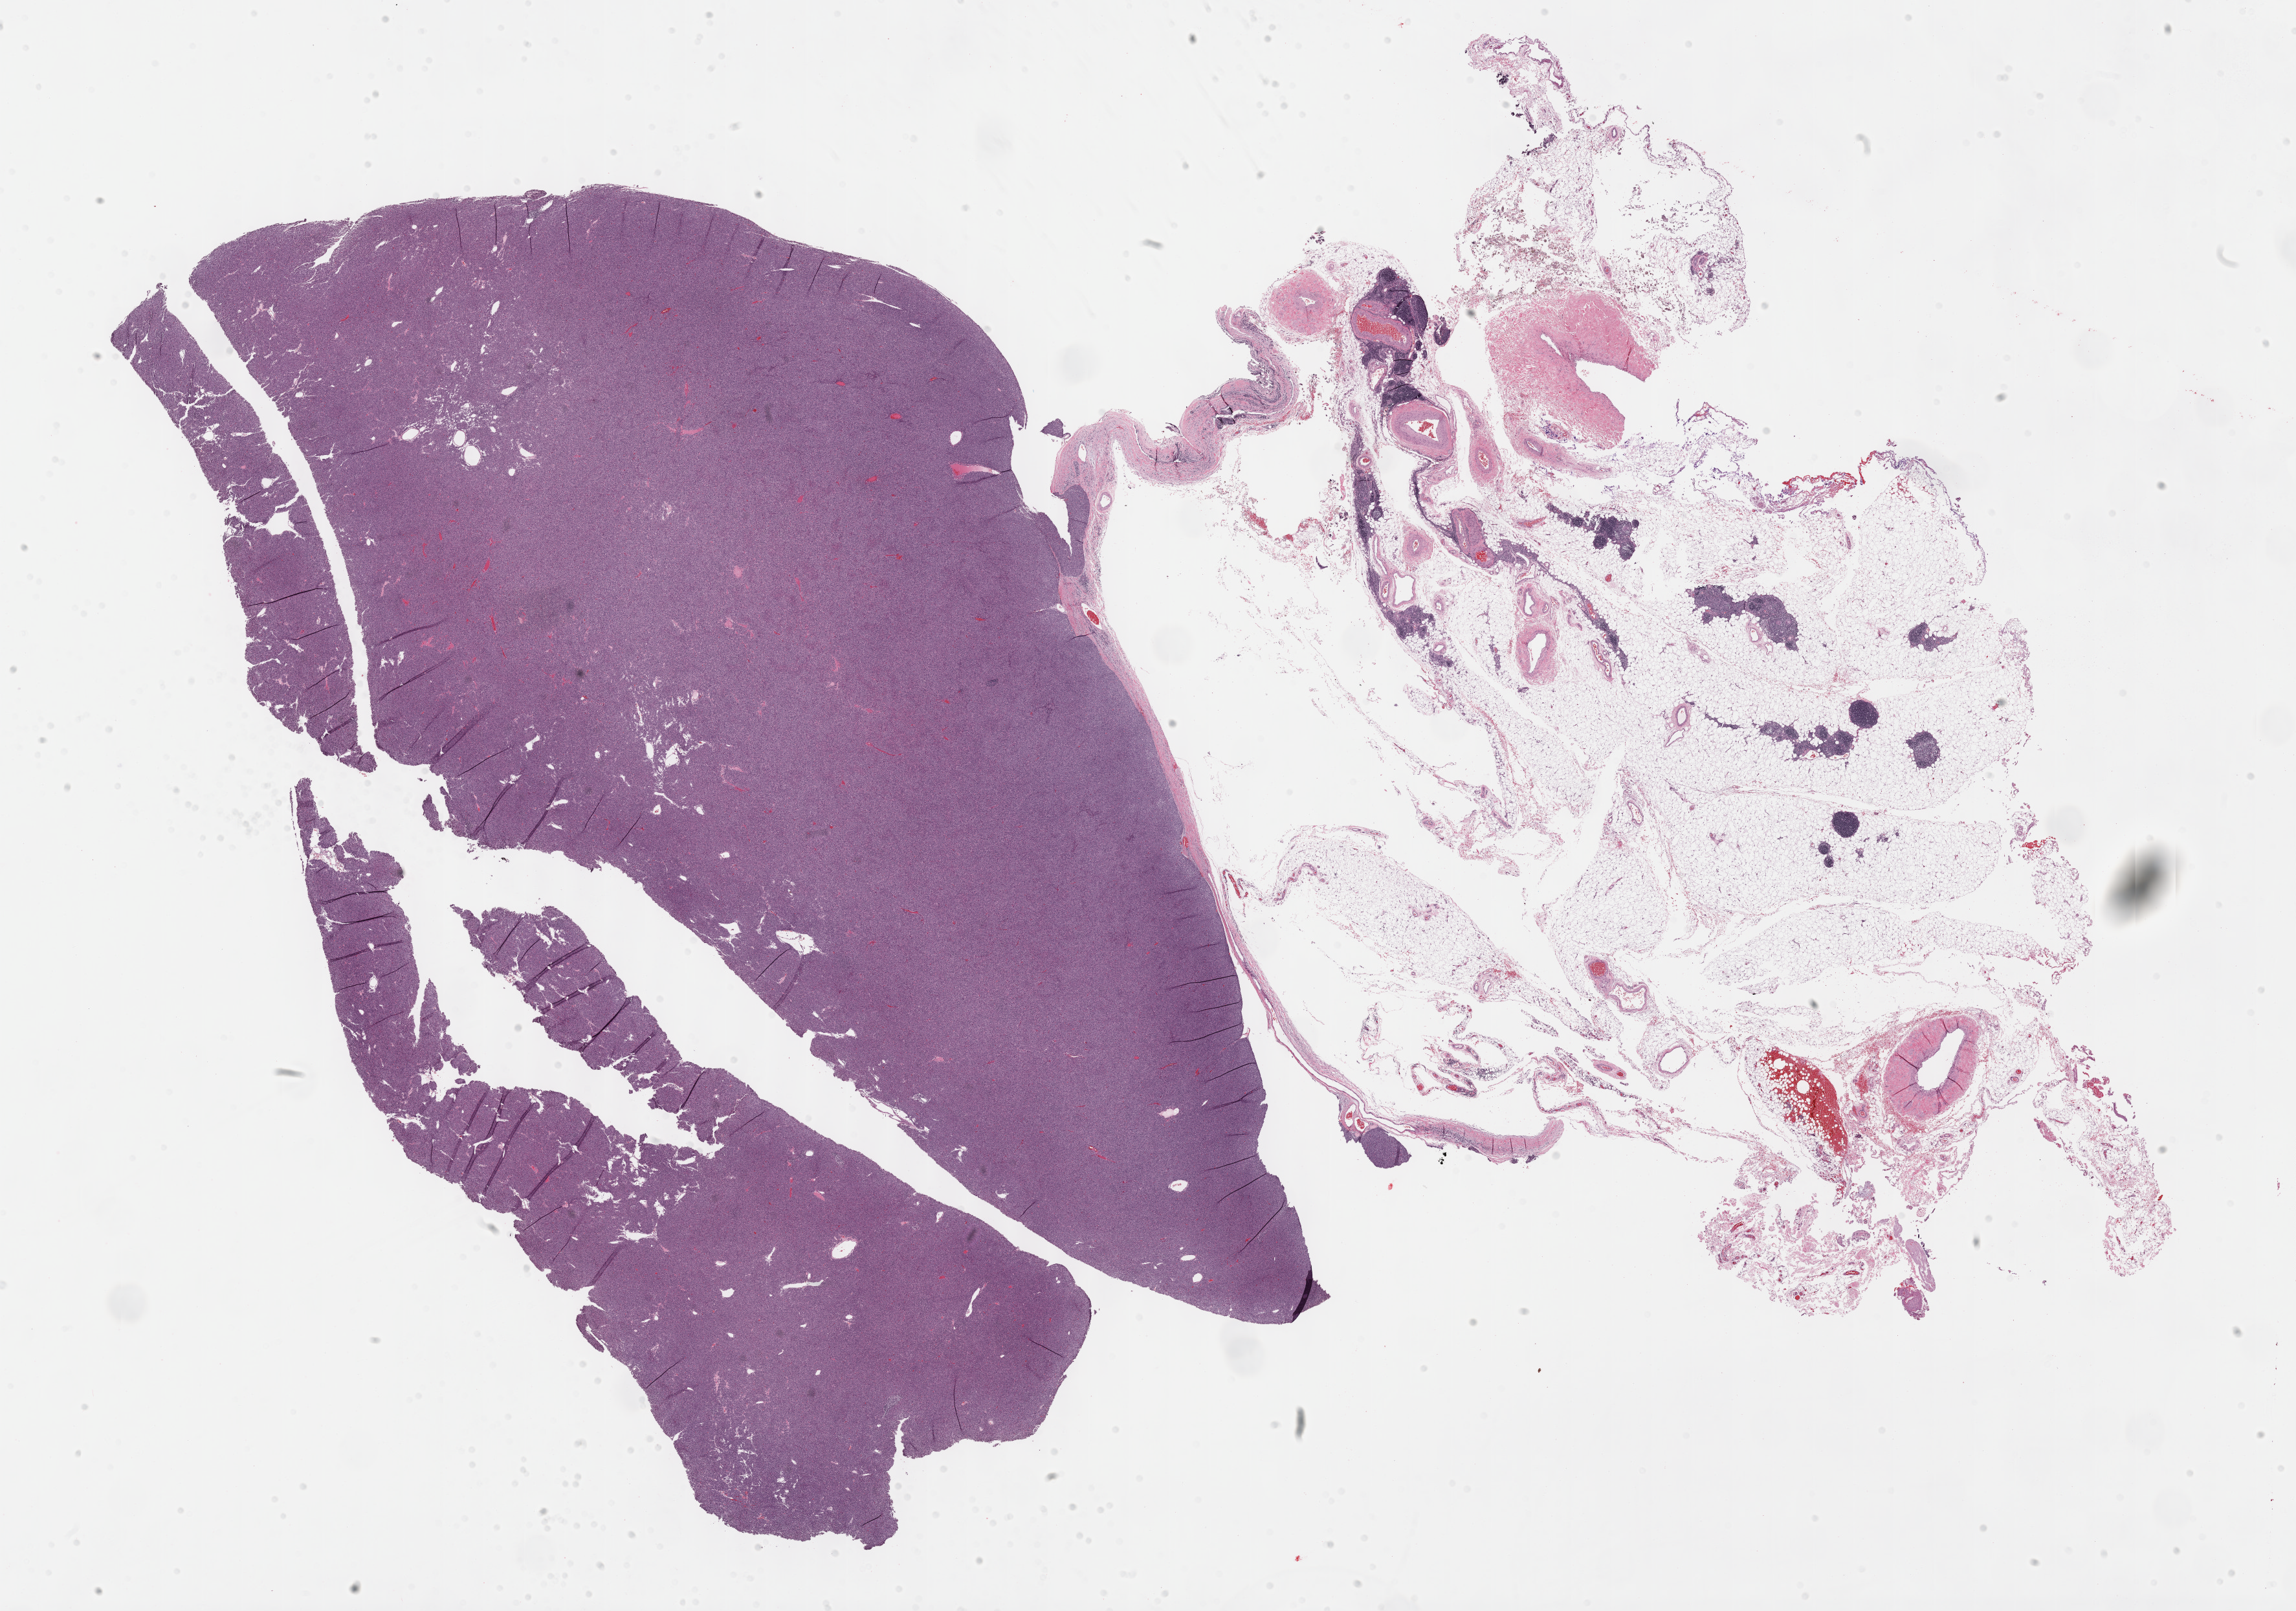
H&E-stained whole-slide image — shown as a low-resolution overview of the whole scanned area (about 28.7 x 20.1 mm), formalin-fixed paraffin-embedded (FFPE) diagnostic section, primary tumour sample from the thymus. Patient: male, age at initial diagnosis 67 years.
Diagnosis: Thymoma, type A, NOS.